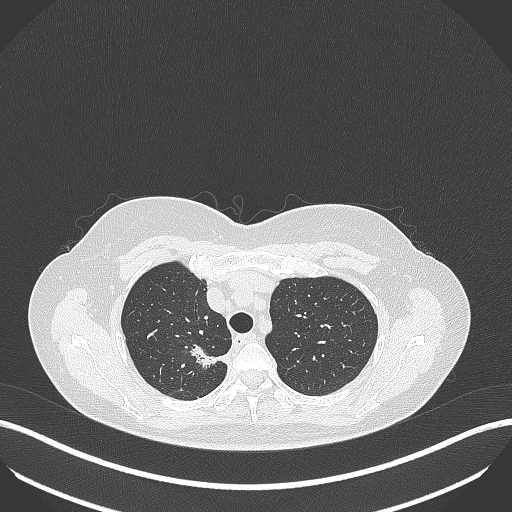
Chest CT, one axial slice; position 311 of 386 along the scan axis; reconstruction kernel B70f; 120 kVp; lung window (W 1500 / L -600 HU); 1 mm slice thickness; 512 × 512 image matrix, field of view 400 × 400 mm. Patient: female, 65 years. From the clinical record (not read from this slice): clinical TNM (as recorded): T1b N0 M0; histopathological grade: G2.
Structures marked on this image (rectangle marked by the reading radiologist):
- lung tumour (recorded histology: adenocarcinoma): bounding box (x1, y1, x2, y2) in pixels: (187, 343, 231, 375)